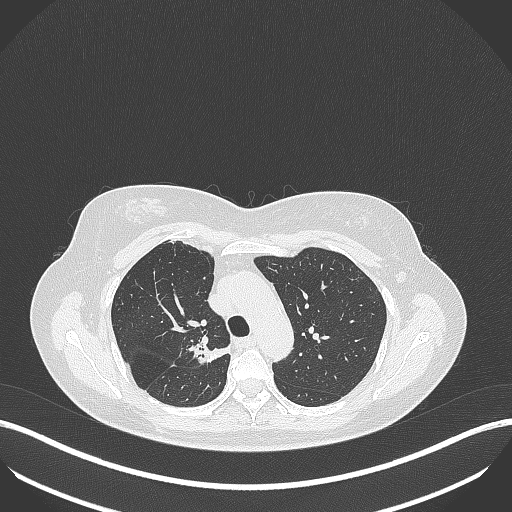
Chest CT, one axial slice. Position 283 of 386 along the scan axis. 120 kVp. Lung window (W 1500 / L -600 HU). 1 mm slice thickness. 512 × 512 image matrix, field of view 400 × 400 mm. Female patient, age 65 years. Case-level facts recorded for this patient, not image findings: clinical TNM (as recorded): T1b N0 M0.
Outlined on this slice (rectangle marked by the reading radiologist):
- lung tumour (recorded histology: adenocarcinoma): box from (x=181, y=339) to (x=232, y=366) px